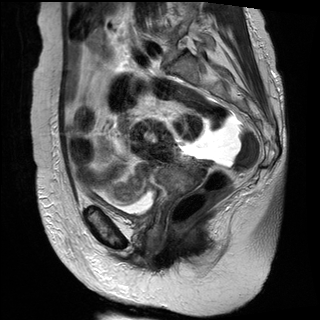
Pelvic MRI for cervical cancer, one sagittal slice; slice 17 of 30 in the series (ordered by position); T2-weighted; 1.5 T; TE 89 ms, TR 2930 ms; 4 mm slice thickness; 320 × 320 image matrix, field of view 260 × 260 mm. Female patient, age 61 years.
Structures marked on this image (manually delineated by an expert):
- uterus and cervix: bounding box <131,119,204,202> (left, top, right, bottom; pixels)